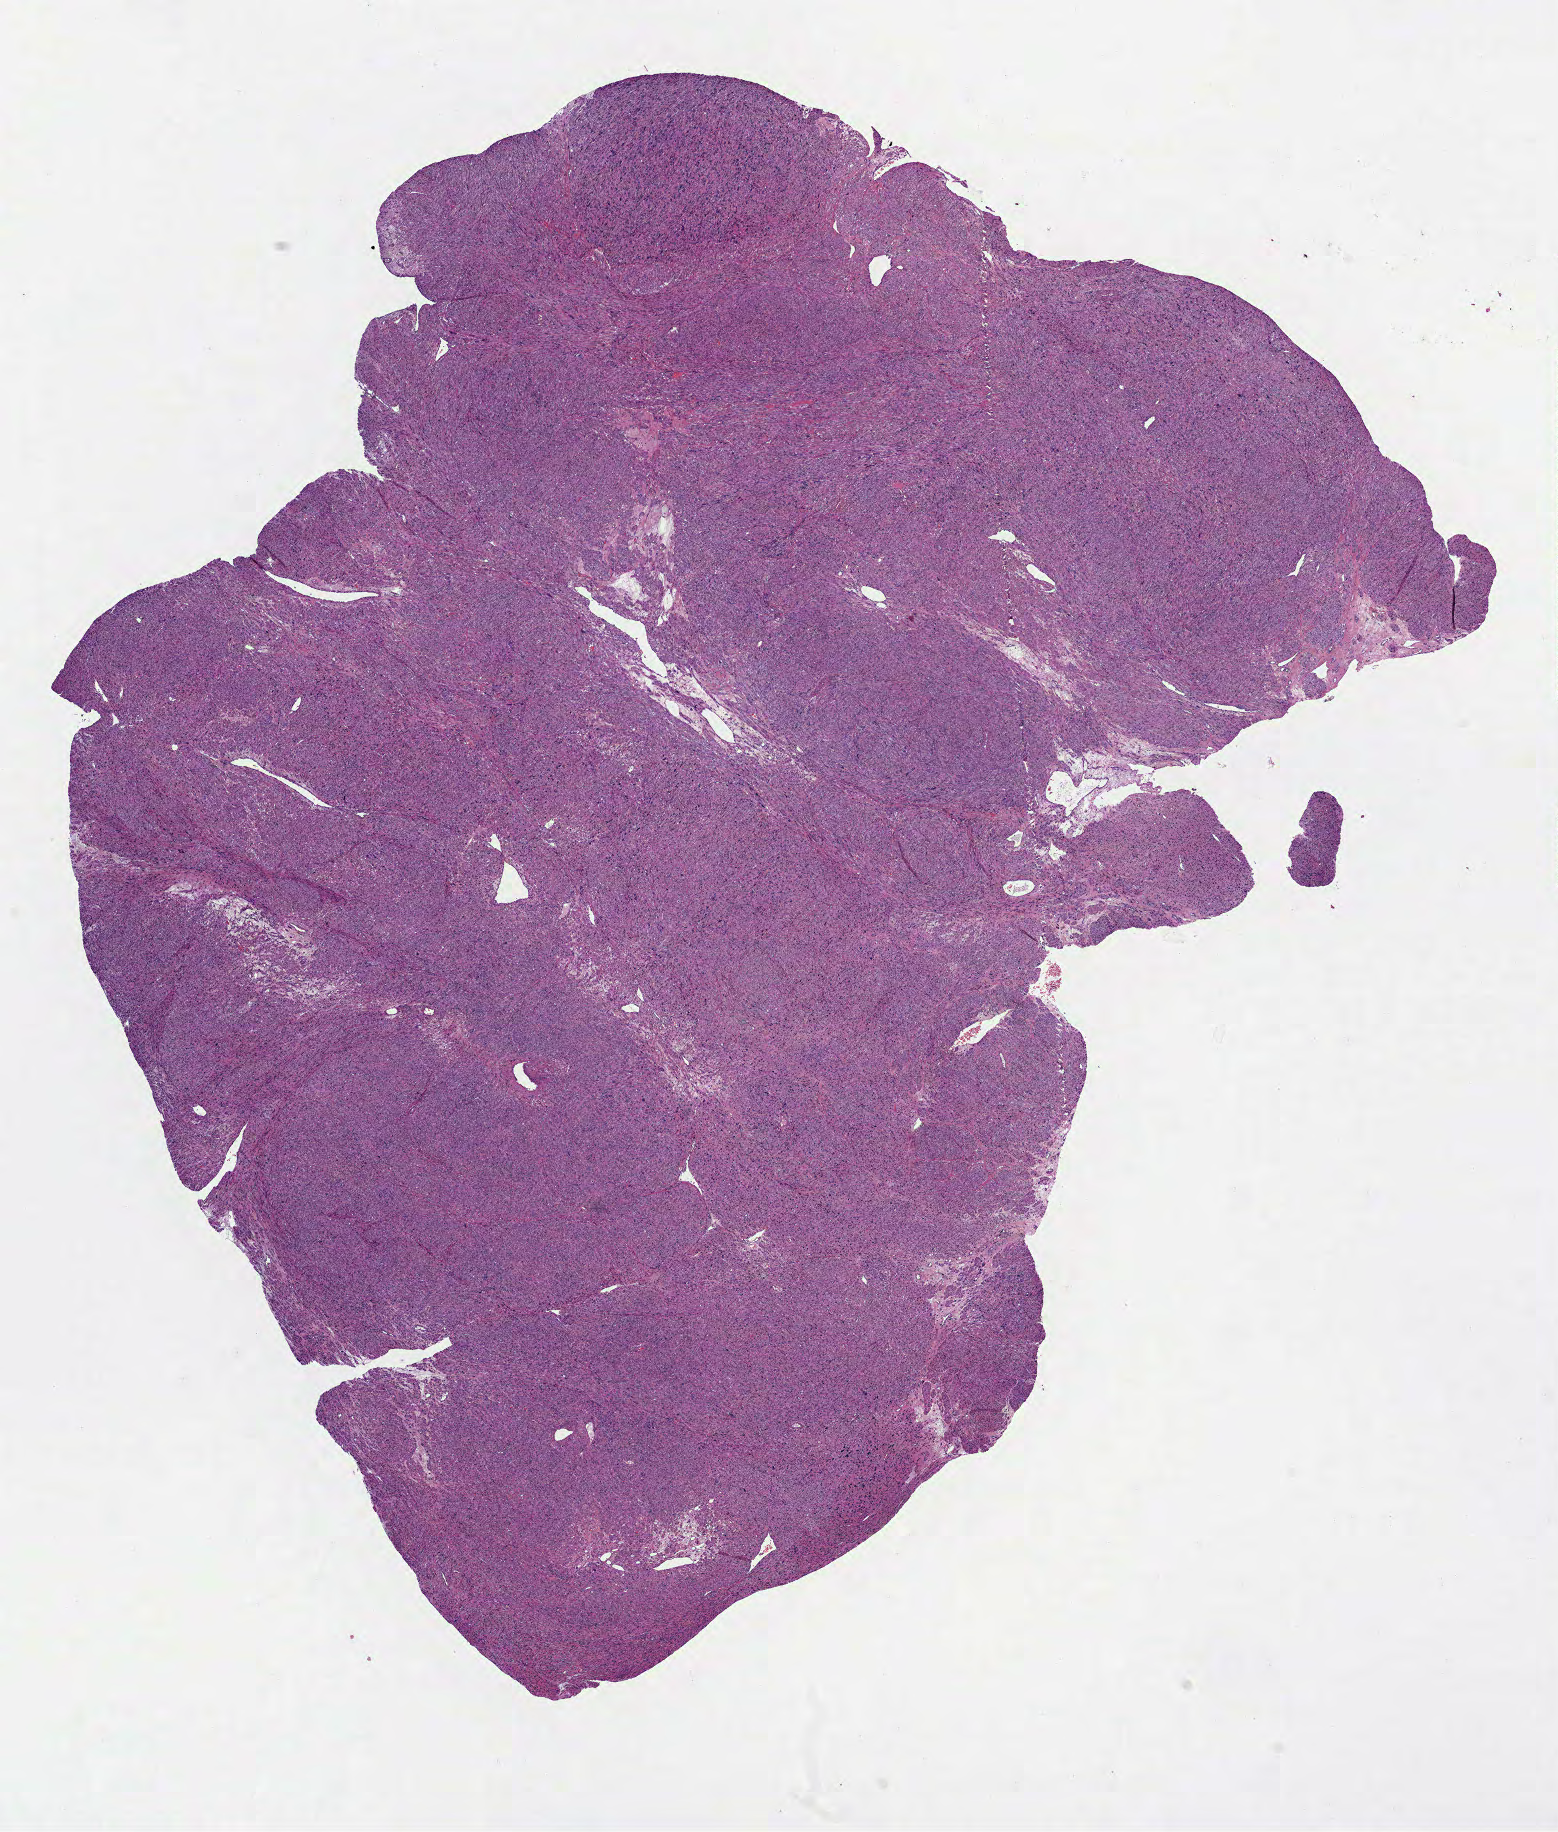
Digitized Hematoxylin and eosin (H&E) stained tissue section (whole slide), a low-resolution overview of the entire scanned area, about 12.6 x 14.8 mm; formalin-fixed paraffin-embedded (FFPE) diagnostic section; uterus, primary tumour sample. Female patient; age at initial diagnosis 49 years.
Pathologic diagnosis: Leiomyosarcoma, NOS.